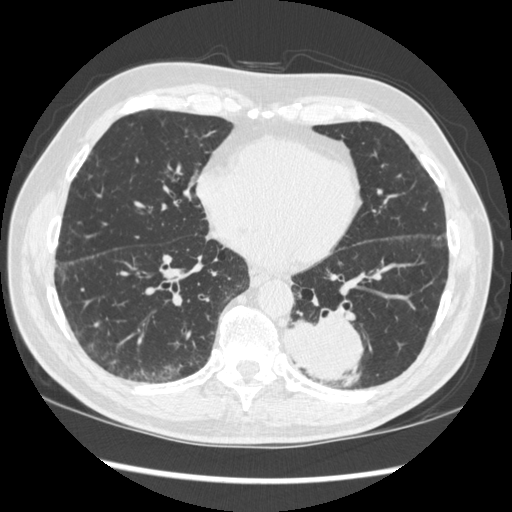
Low-dose screening chest CT, axial slice; baseline annual screen; lung window (W 1500 / L -600 HU); 120 kVp; slice 124 of 348 in the series. Male, age 72 years at enrolment. Current smoker at enrolment.
Lesion marked by an expert reader, bounding box [x1, y1, x2, y2] px = [273, 297, 377, 386]. The screening reader recorded 2 non-calcified nodules or masses ≥4 mm on this exam (left lower lobe, right middle lobe); which of them this box marks is not recorded. Official screen result: positive, change unspecified: nodule(s) >= 4 mm or enlarging nodule(s), mass(es), or other non-specific abnormalities suspicious for lung cancer. Later outcome: lung cancer diagnosed 37 days after this screen — squamous cell carcinoma, NOS, left lower lobe, stage IIIA (AJCC 6th edition), 60 mm at pathology.